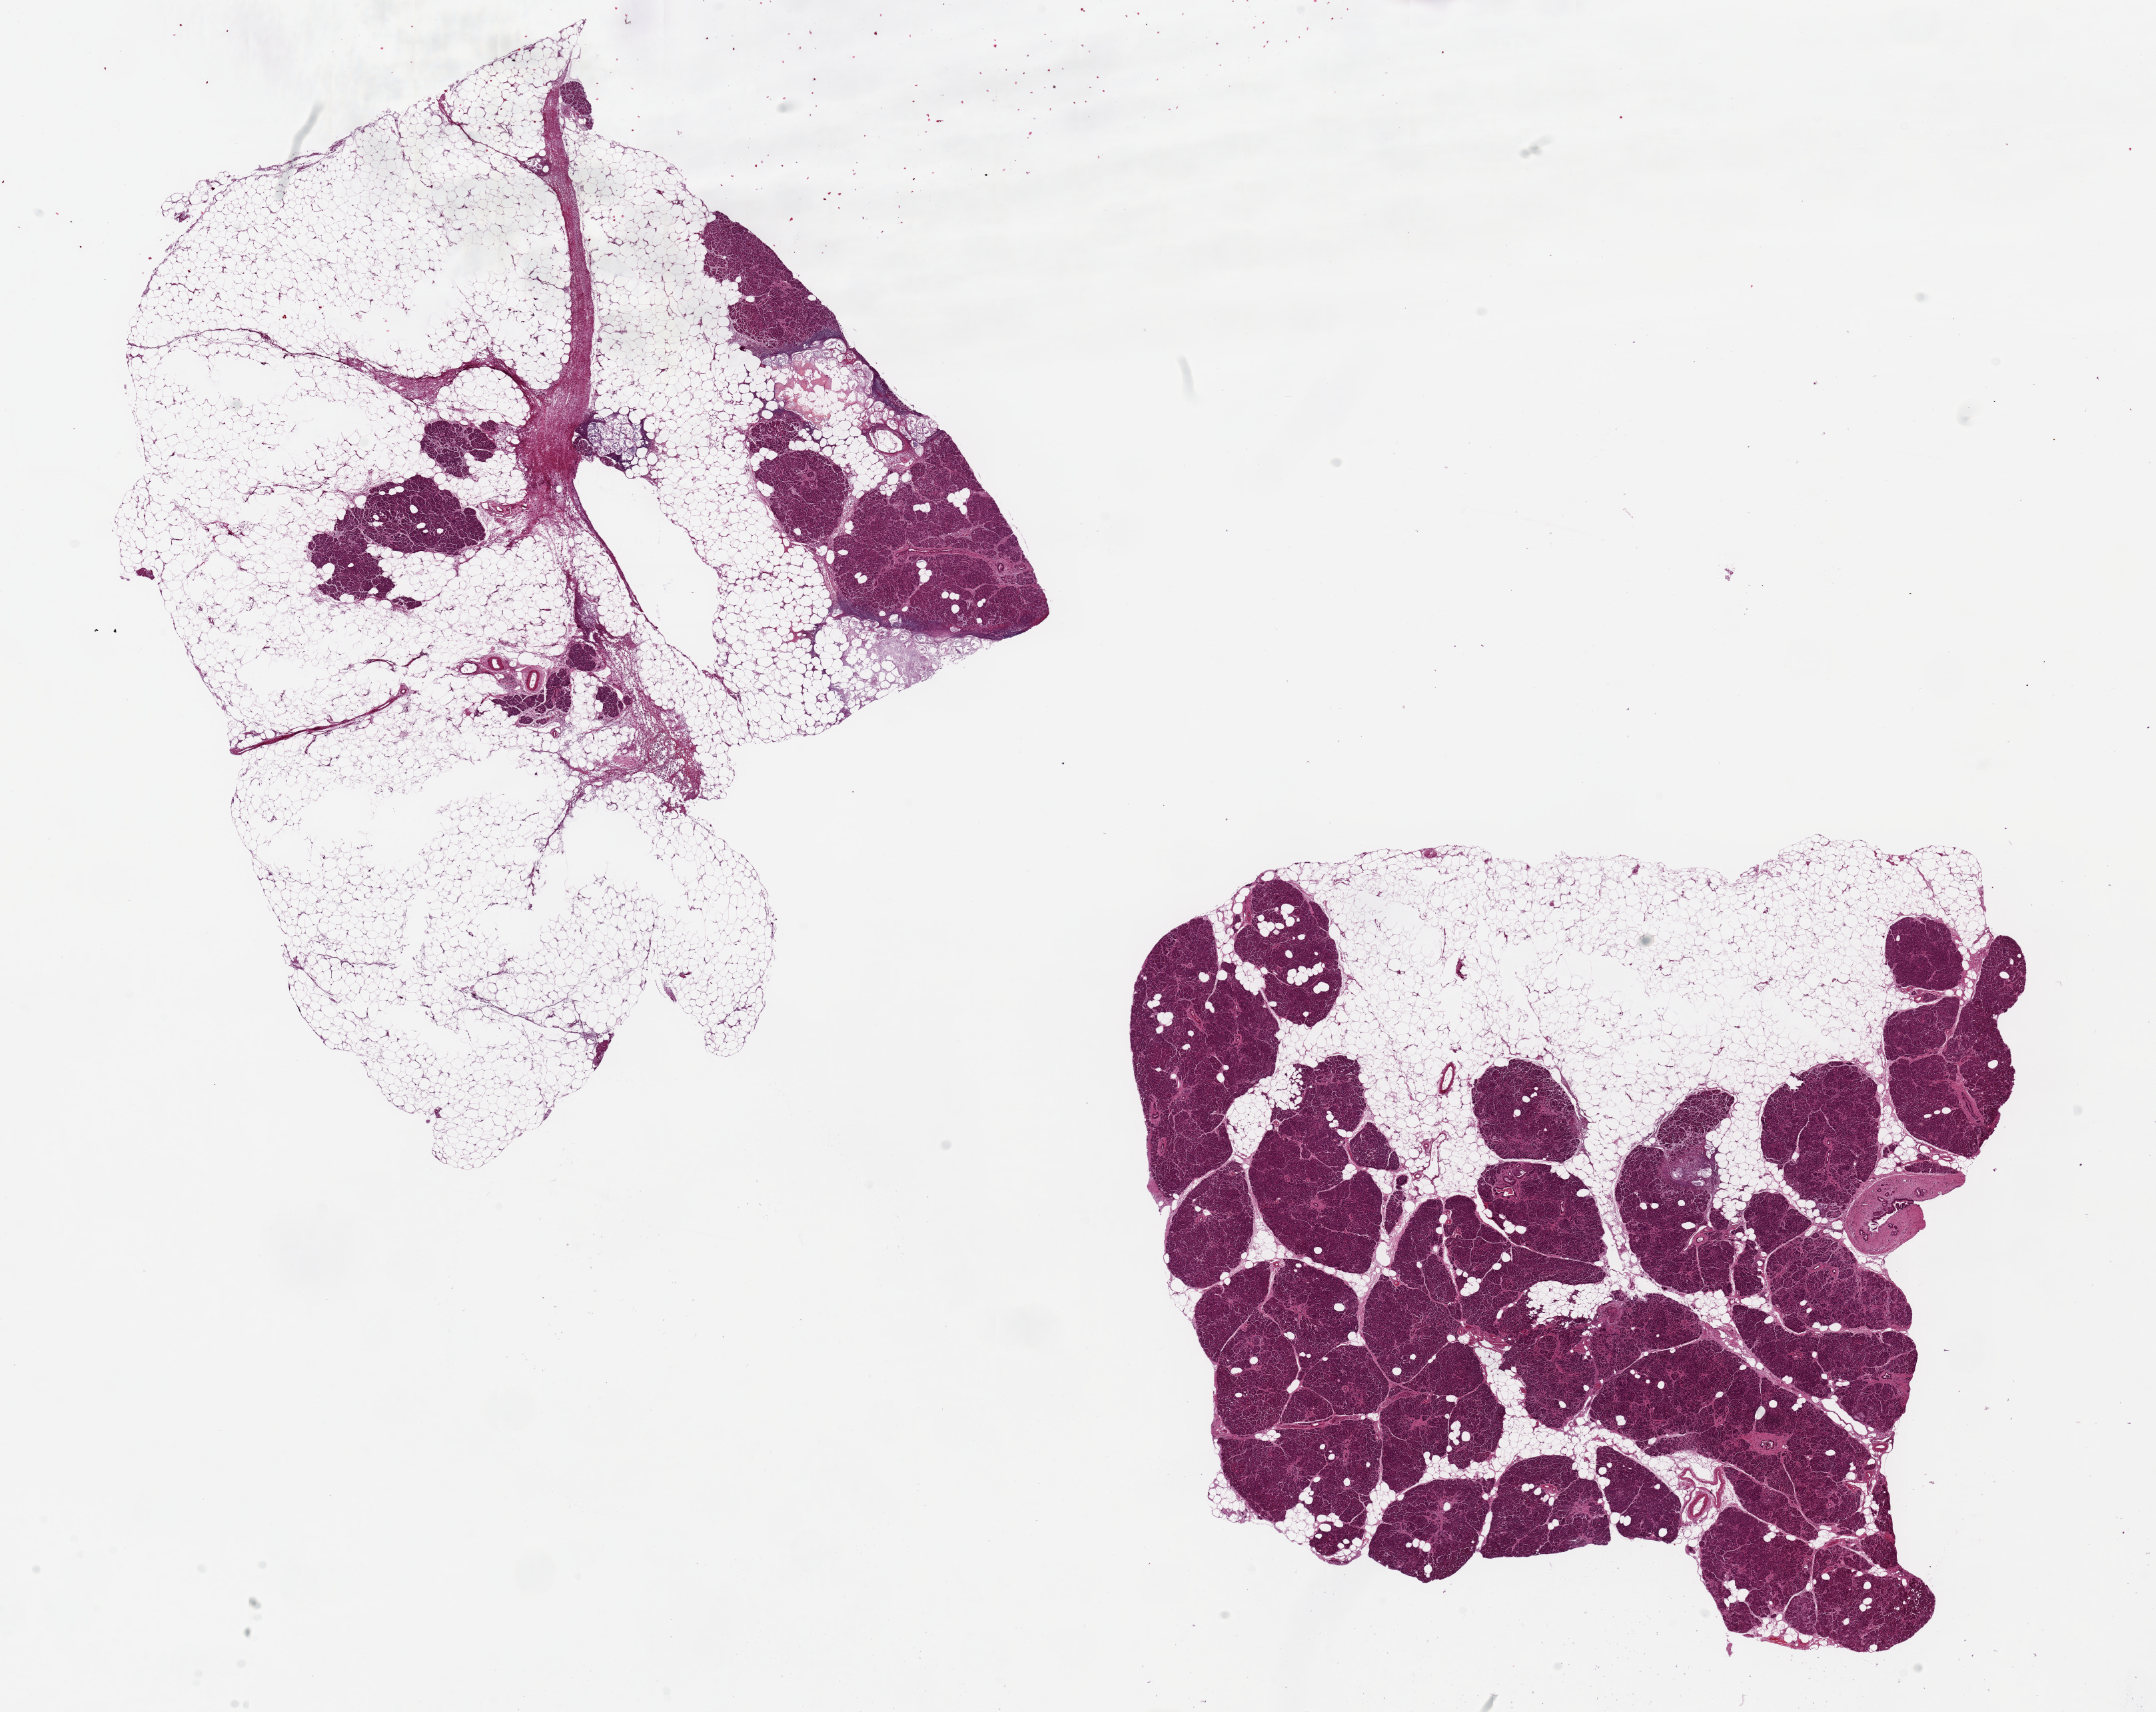
Digitized haematoxylin and eosin-stained section, shown as a low-resolution overview of the whole scanned area (about 25.6 x 20.3 mm). PAXgene-fixed paraffin-embedded (PFPE) section. Target tissue: pancreas. Tissue donor sample.
Pathologist's review note for this sample: 2 pieces, one ~9x9mm with attached 7x3mm adherent/interstital fat; the other ~6x2mm with adherent 11x6mm fat; Parenchyma well preserved, few Islets seen; Patchy fibrosis.